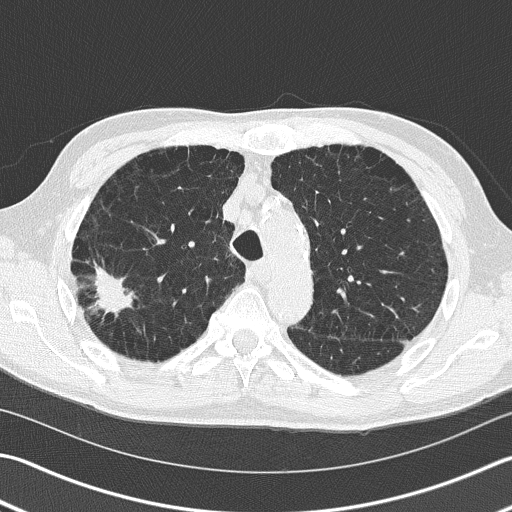
Axial slice from a low-dose chest CT screening exam; baseline annual screen; lung window (W 1500 / L -600 HU); 2 mm slice thickness; slice 49 of 163 in the series. Male, age 66 years at enrolment. Current smoker at enrolment.
• Lesion marked by an expert reader, bounding box <68,249,138,339> (left, top, right, bottom; pixels).
• Screening reader's record for this exam (one nodule recorded; not confirmed to be the boxed lesion): non-calcified nodule or mass ≥4 mm, right upper lobe, 39 × 23 mm, spiculated (stellate) margins, soft tissue attenuation.
• Participant outcome: lung cancer diagnosed 36 days after this screen — squamous cell carcinoma, NOS, right upper lobe, poorly differentiated (G3), stage IB (AJCC 6th edition), 23 mm at pathology.